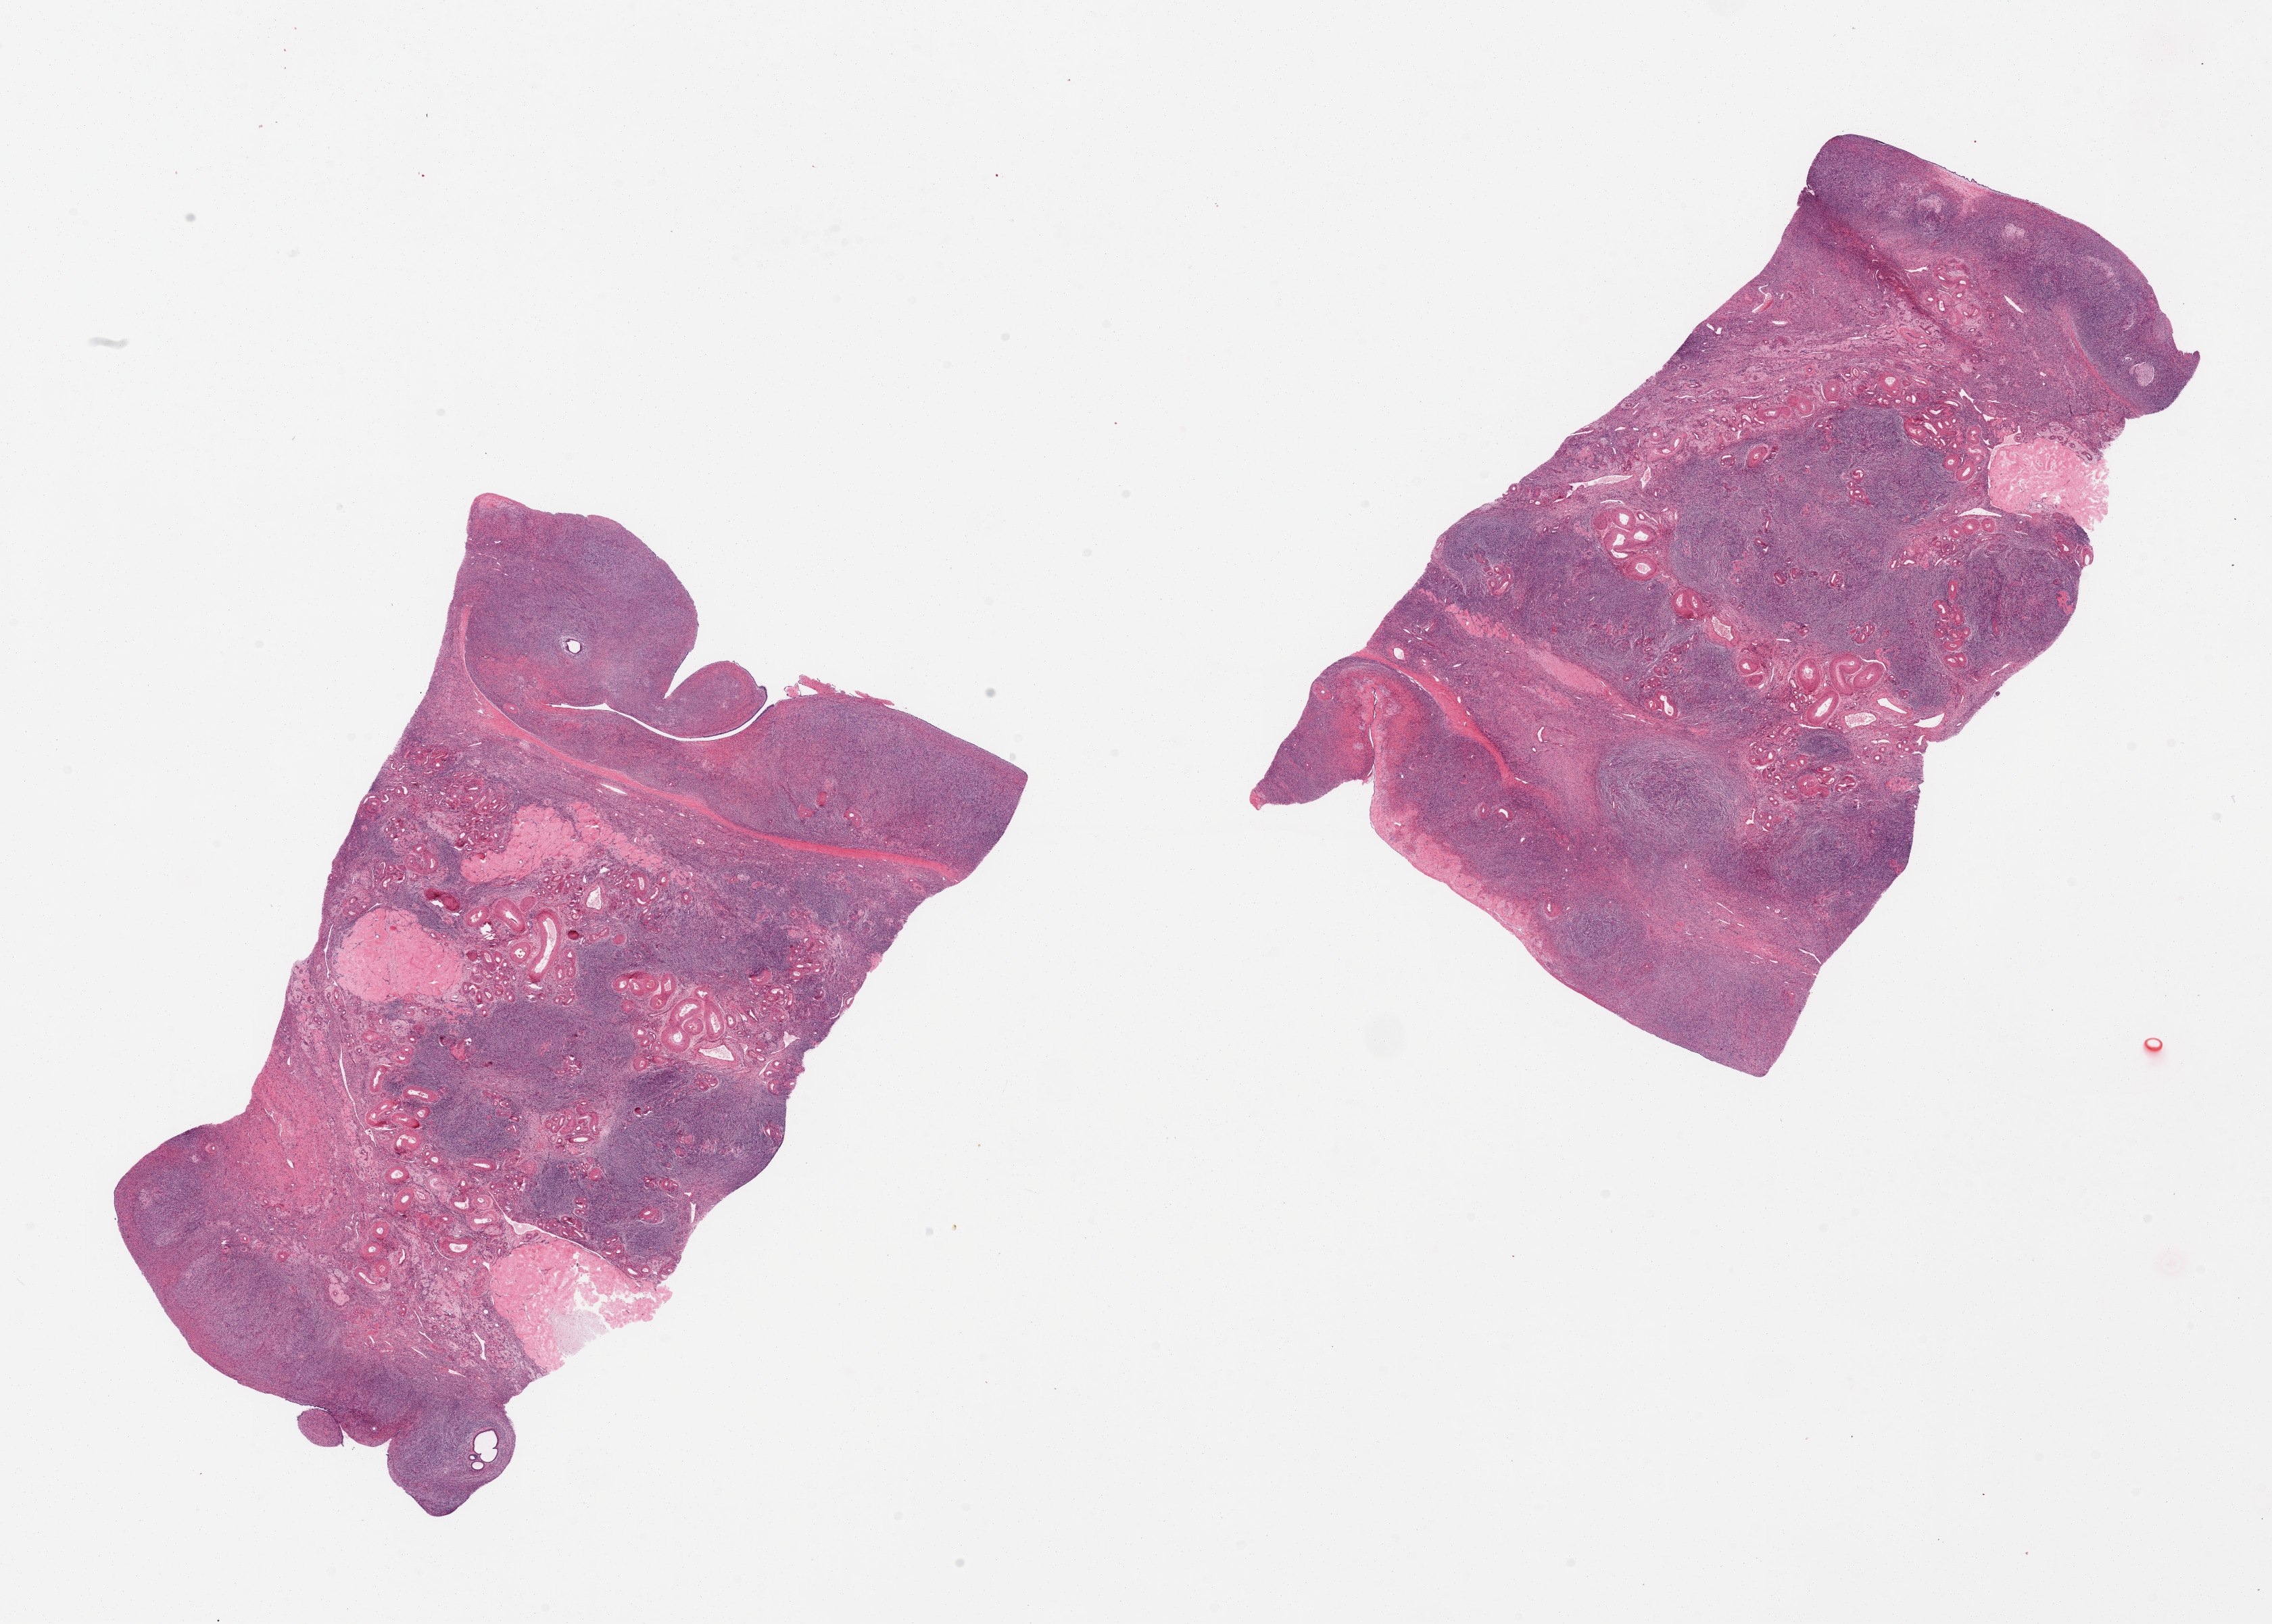
Haematoxylin and eosin whole-slide image, a low-resolution overview of the entire scanned area, about 26.6 x 19.0 mm. PAXgene-fixed, paraffin-embedded tissue. Sampled site (target tissue): ovary. Tissue donor sample.
- pathologist's review note for this sample: 2 pieces, few epithelial inclusion glands